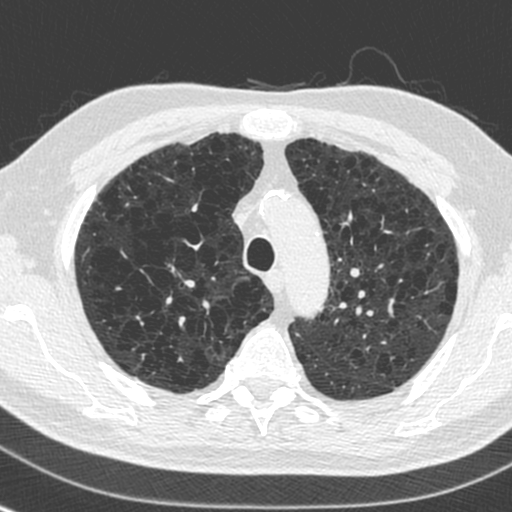
Chest CT (low-dose screening protocol), one axial image; baseline screening round; lung window (W 1500 / L -600 HU); 1.3 mm slice thickness; standard (soft-tissue) reconstruction kernel (C); slice 59 of 250 in the series. Male, age 73 years at enrolment. Current smoker at enrolment.
Lesion marked by an expert reader, box from (x=156, y=251) to (x=202, y=288) px. Screening reader's record for this exam: no non-calcified nodule ≥4 mm recorded. Lung cancer was diagnosed 446 days after this screen (after the second annual screen): squamous cell carcinoma, NOS, right upper lobe, stage IA (AJCC 6th edition), 10 mm at pathology.